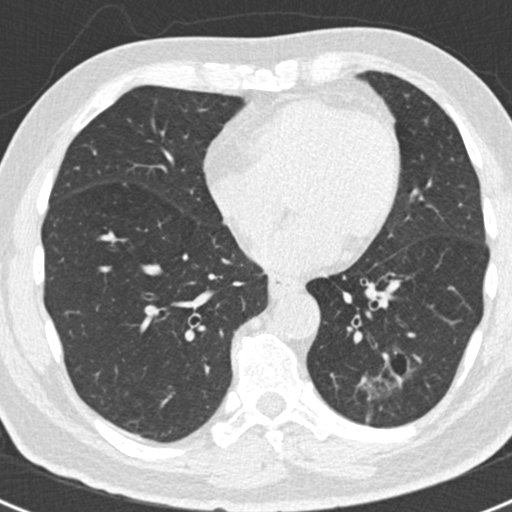
Low-dose screening chest CT, axial slice, first (baseline) screen, lung window (W 1500 / L -600 HU), 2 mm slice thickness, standard (soft-tissue) reconstruction kernel (B30f), 512 × 512 image matrix, field of view 300 × 300 mm. Male participant, aged 66 years at enrolment.
Lesion marked by an expert reader, bounding box [x1, y1, x2, y2] px = [342, 337, 420, 415]. Screening reader's record for this exam (one nodule recorded; not confirmed to be the boxed lesion): non-calcified nodule or mass ≥4 mm, left lower lobe, 43 × 27 mm, smooth margins. Participant outcome: lung cancer diagnosed 801 days after this screen — adenocarcinoma, NOS, left lower lobe, poorly differentiated (G3), stage IB (AJCC 6th edition), 38 mm at pathology.